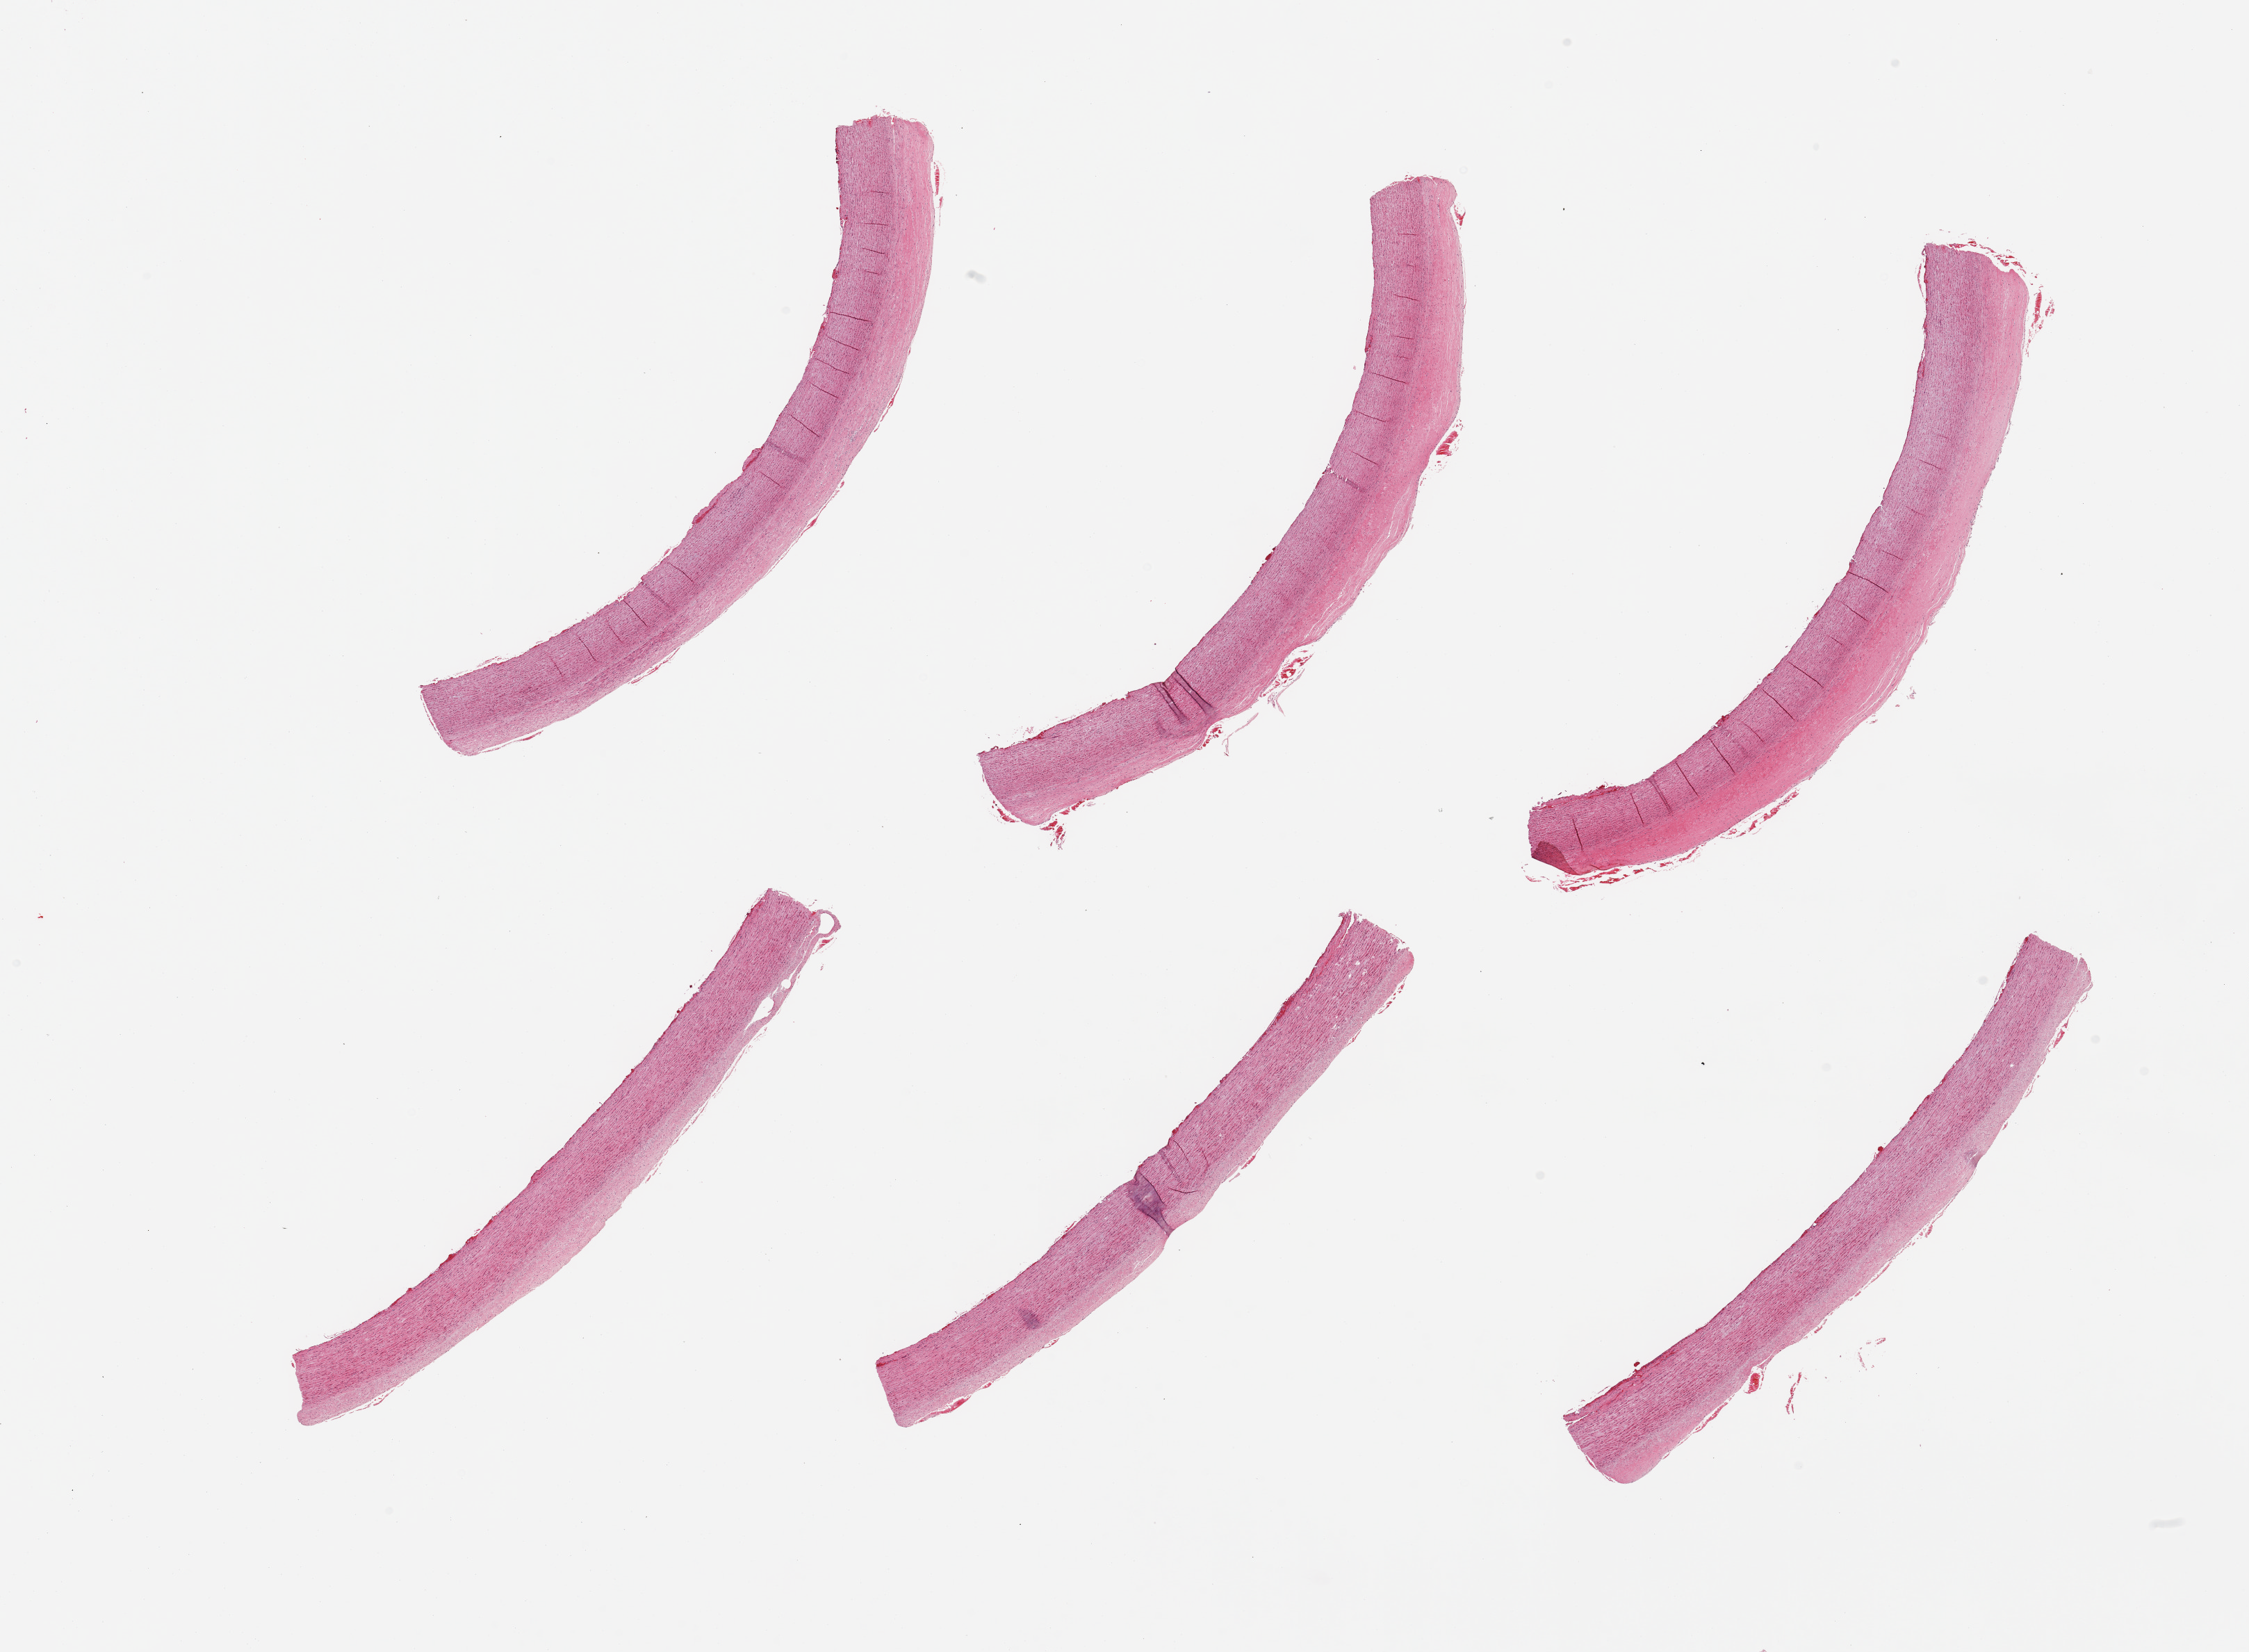
Hematoxylin and eosin (H&E) whole-slide image — whole scanned area (about 25.6 x 18.8 mm) shown as a low-resolution overview; PAXgene-fixed paraffin-embedded (PFPE) section; target tissue: aorta; donor tissue sample. Donor sex: male.
- reviewer comment on this tissue sample: 6 pieces, atherosis layer up to ~0.5mm